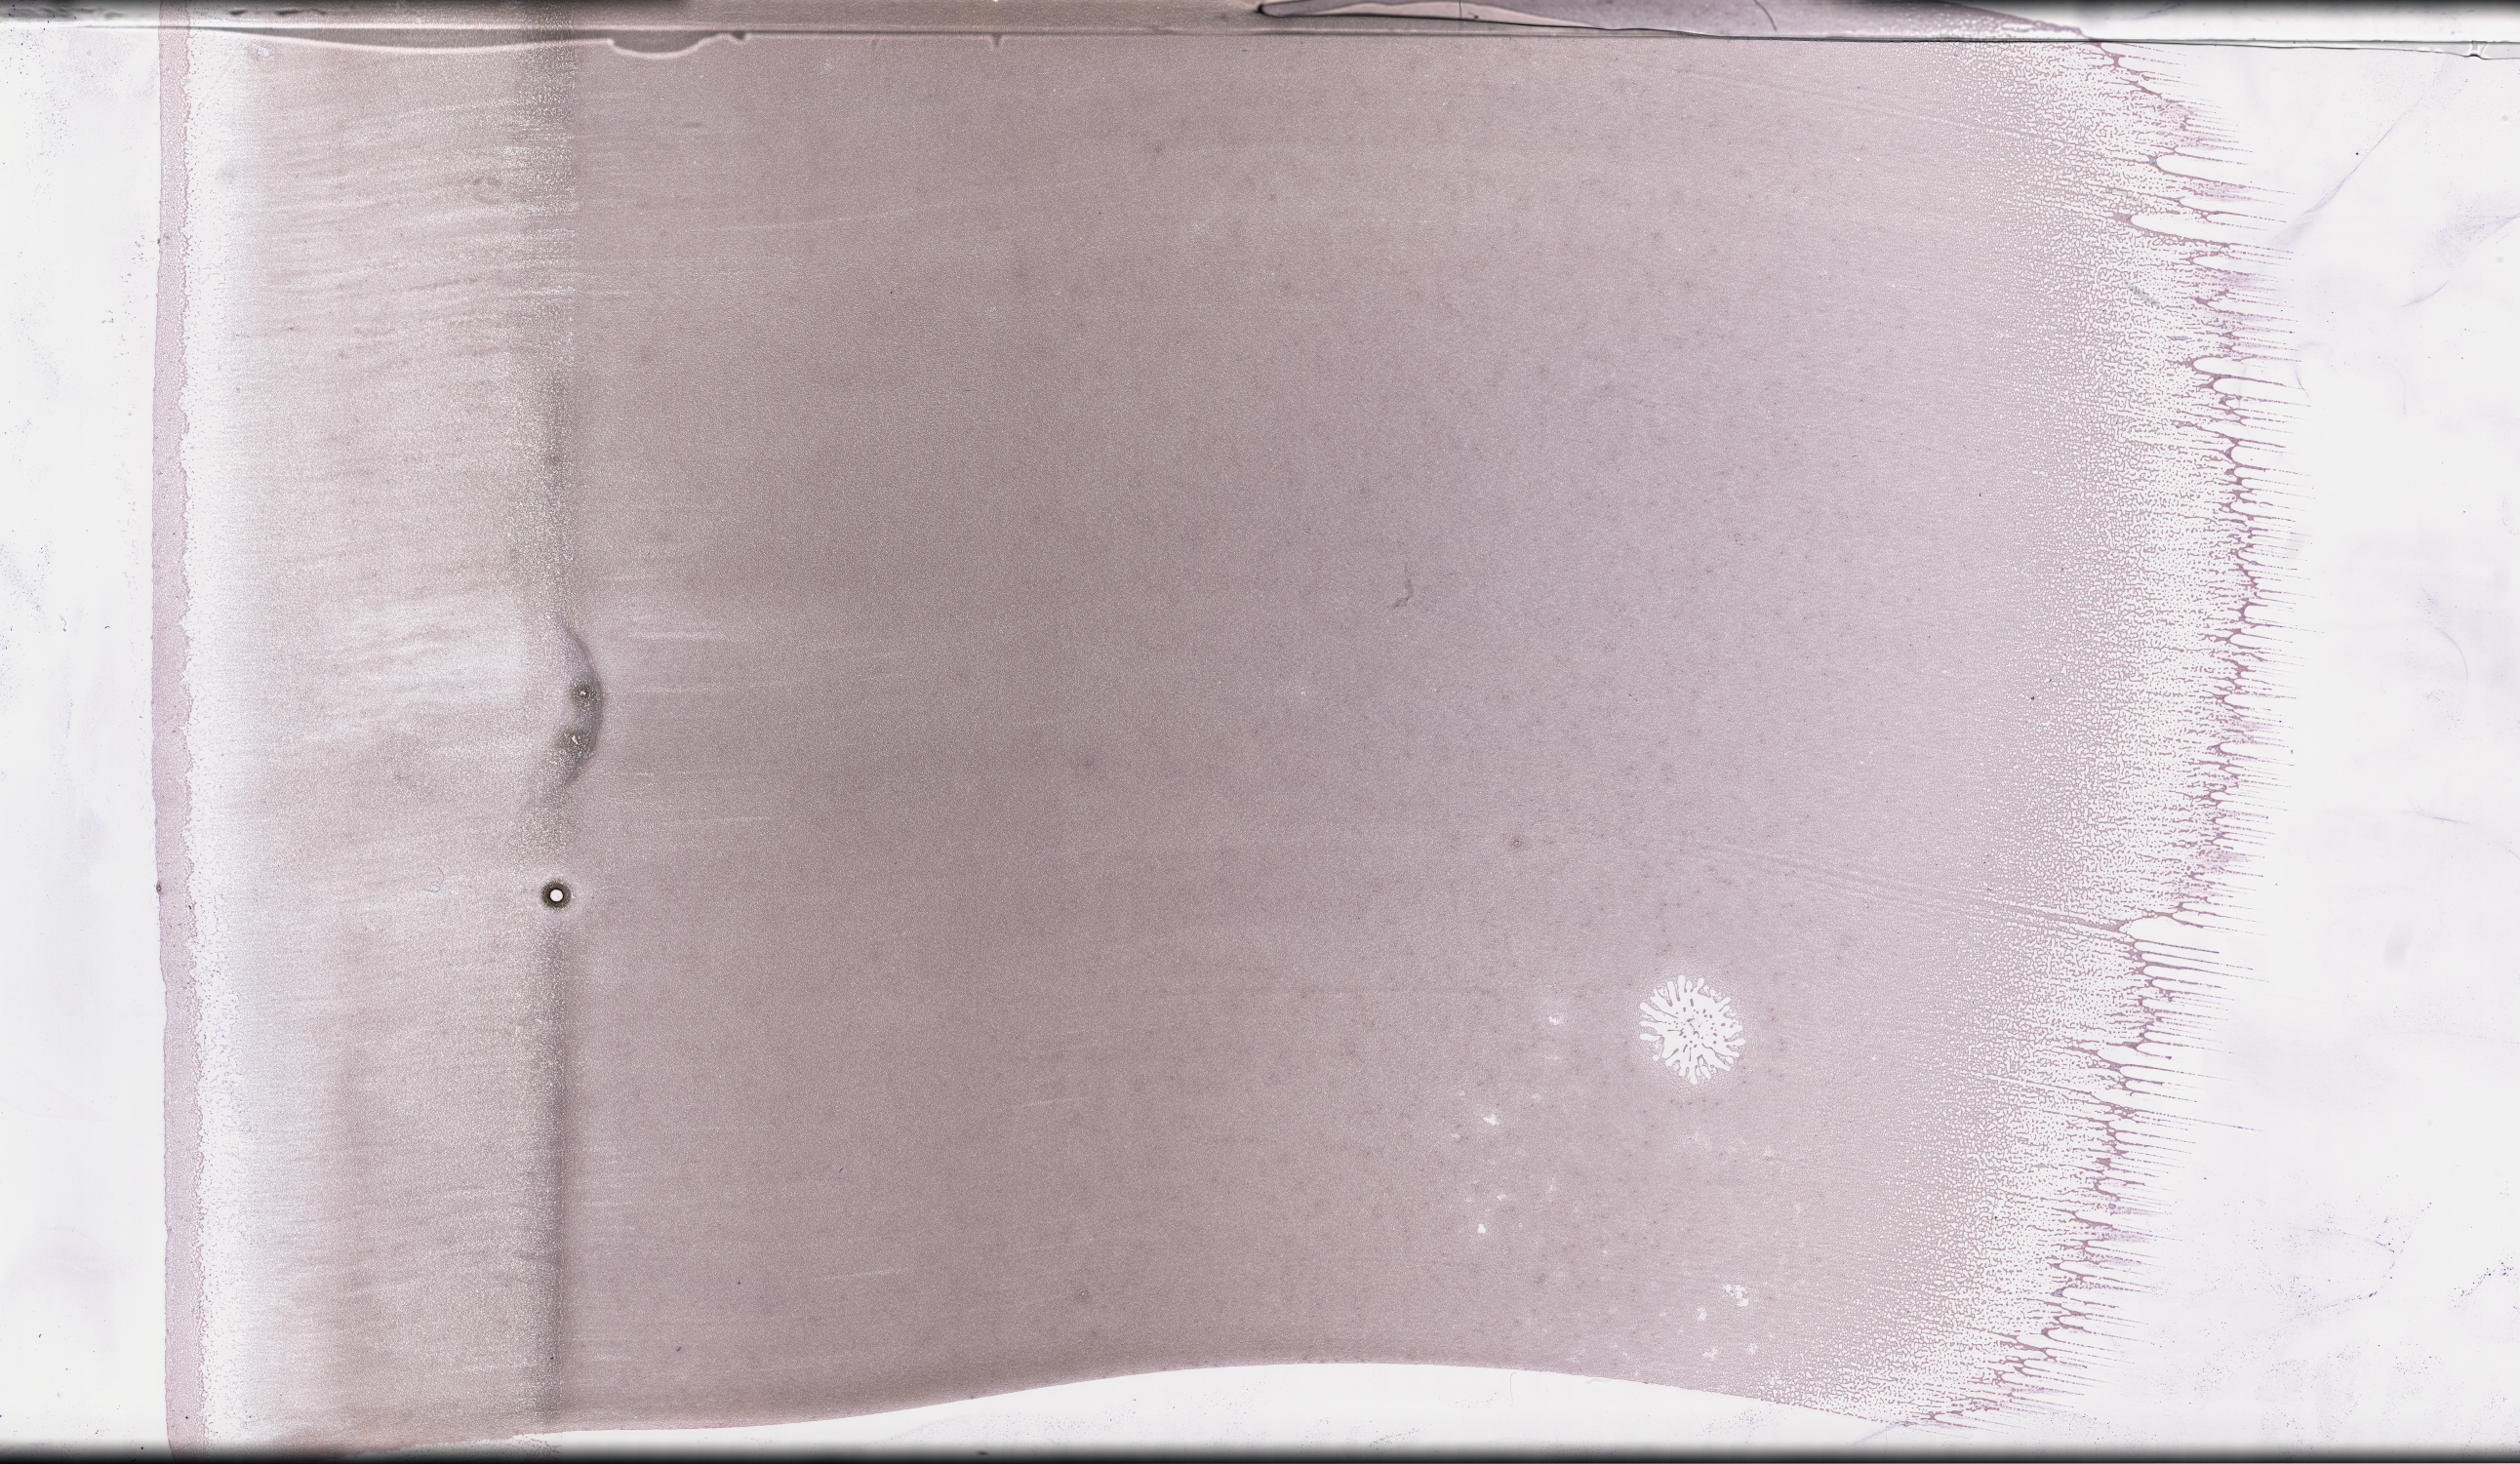
Whole-slide image of a whole blood smear, Wright-Giemsa stain, low-resolution overview of the scanned area, about 41.7 x 24.2 mm, collected on treatment. Patient sex: female.
Patient diagnosis: Plasma Cell Myeloma.